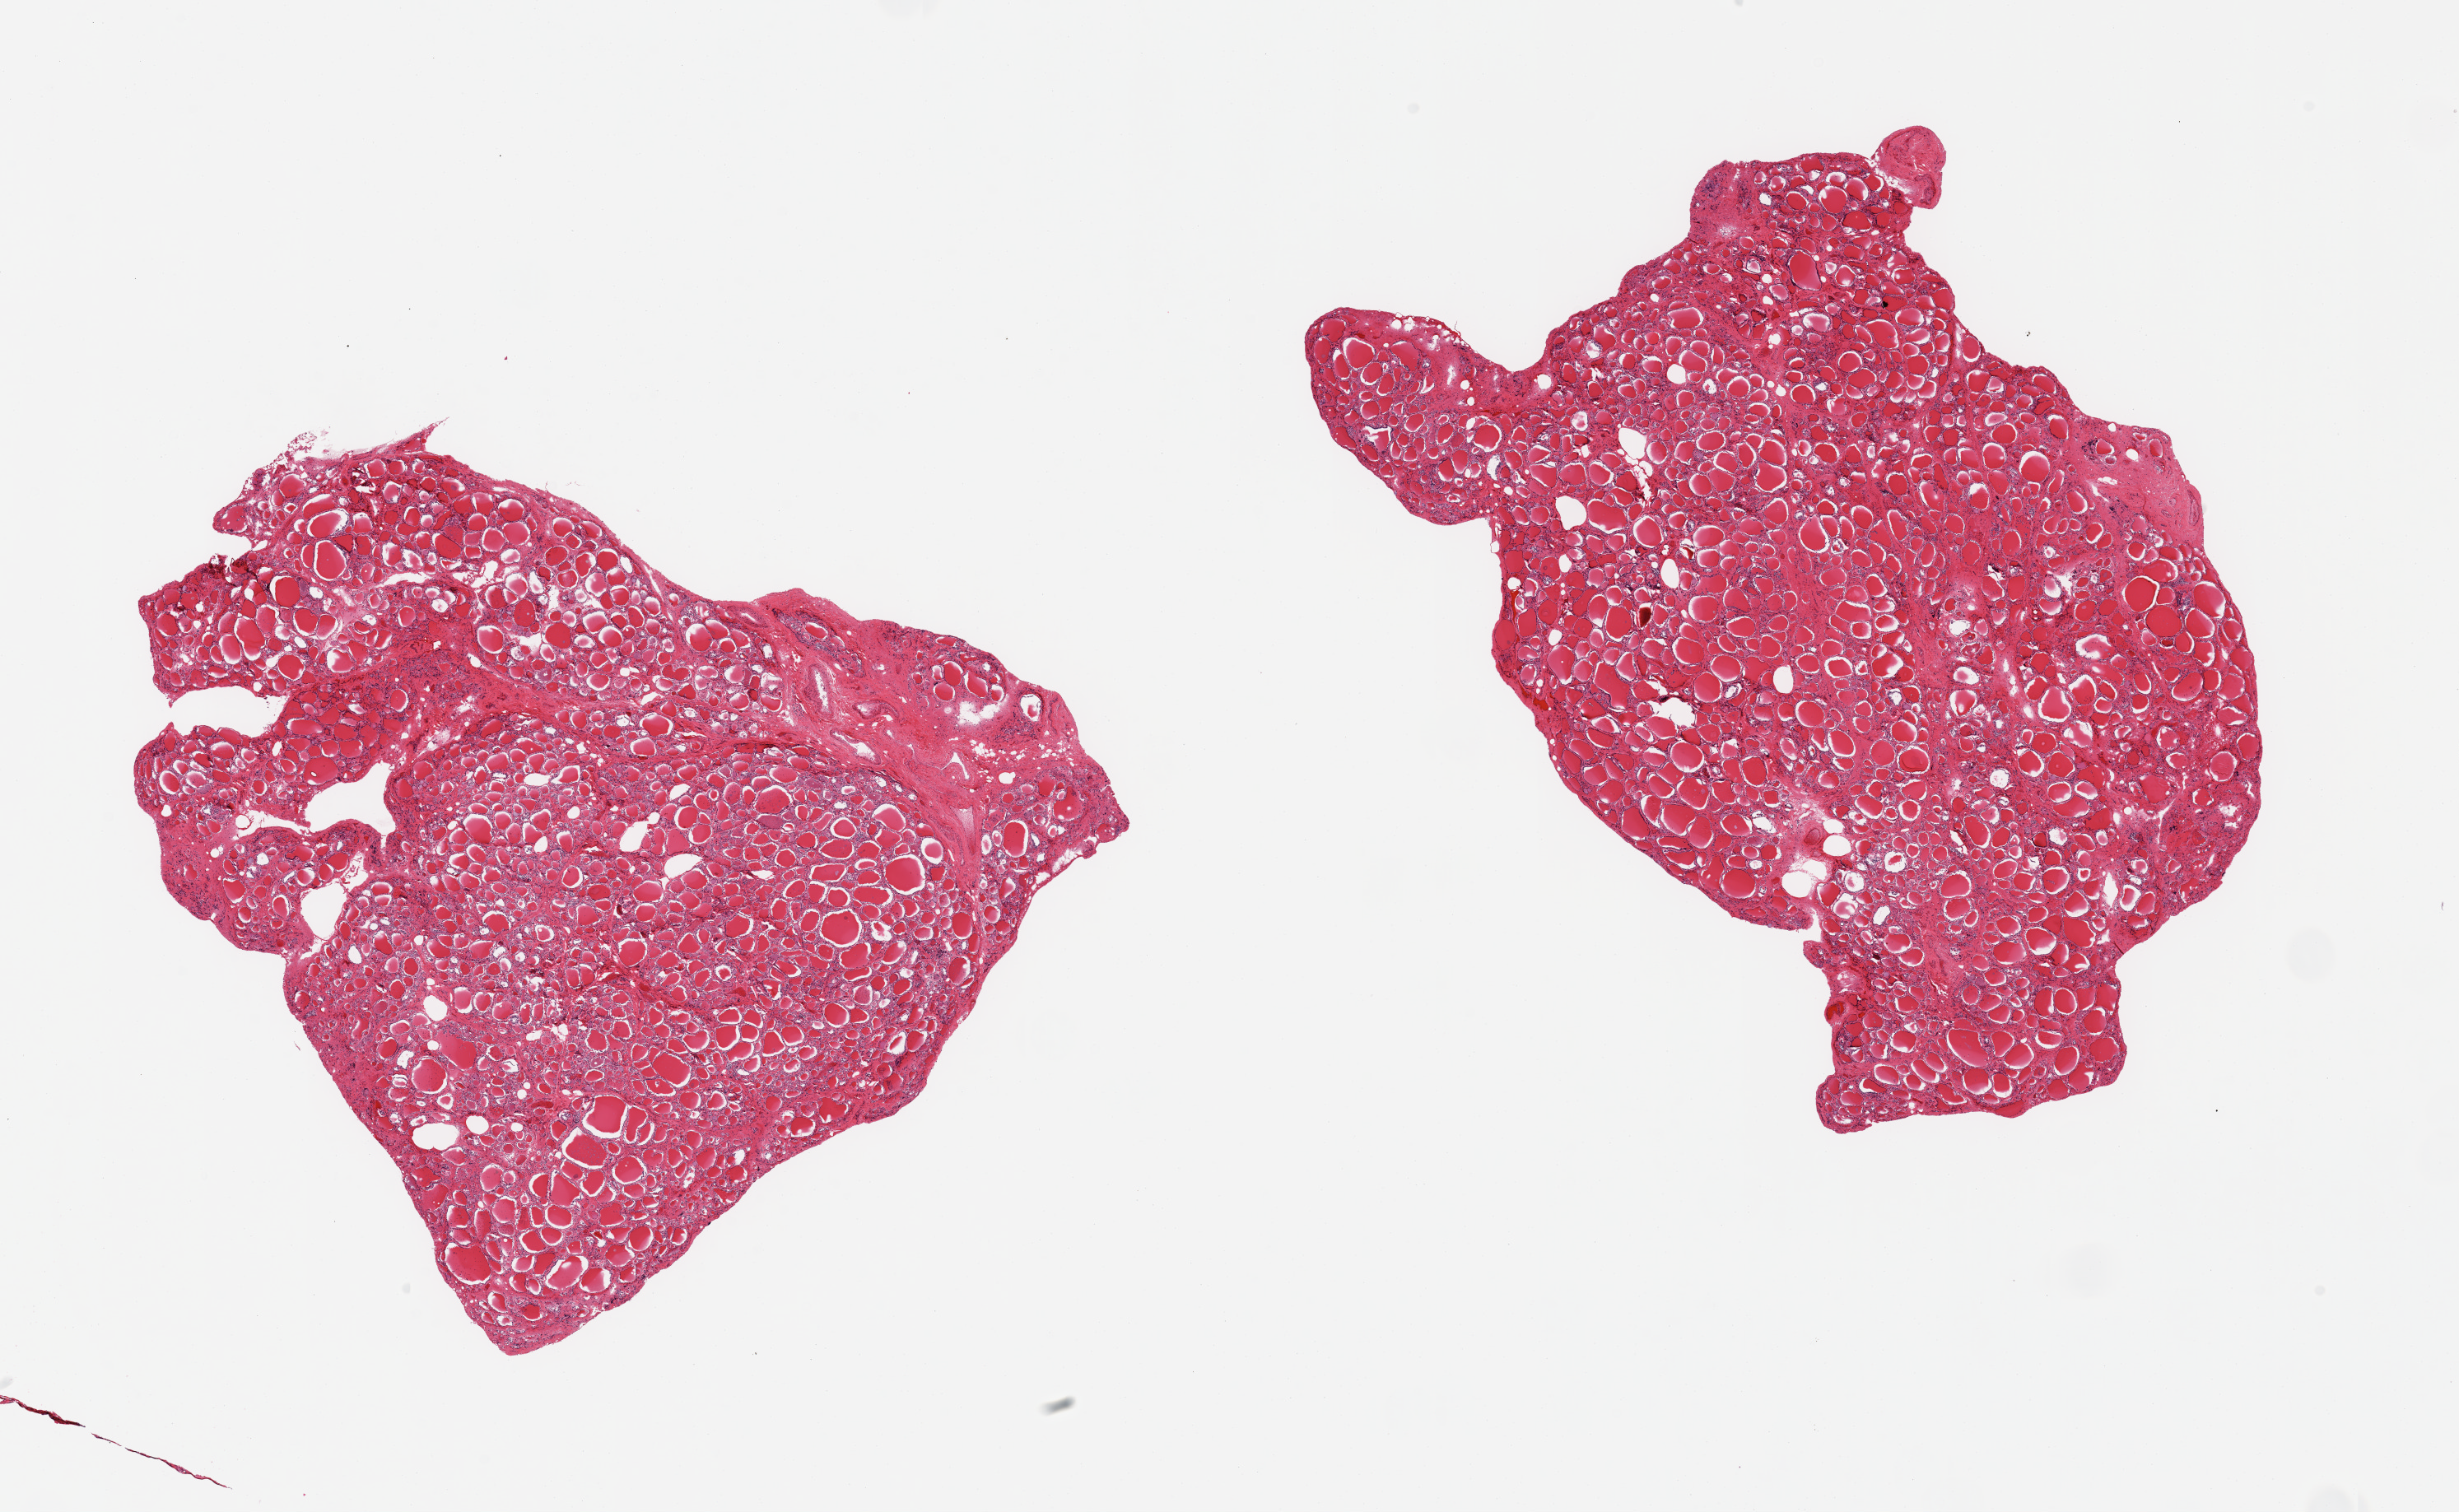
Digitized H&E-stained section, brightfield, shown as a low-resolution overview of the whole scanned area (about 23.6 x 14.5 mm), PAXgene-fixed, paraffin-embedded tissue, sampled site (target tissue): thyroid, donor tissue sample.
Reviewer comment on this tissue sample: 2 pieces; no lesions; 5 & 10% fibrovascular content.